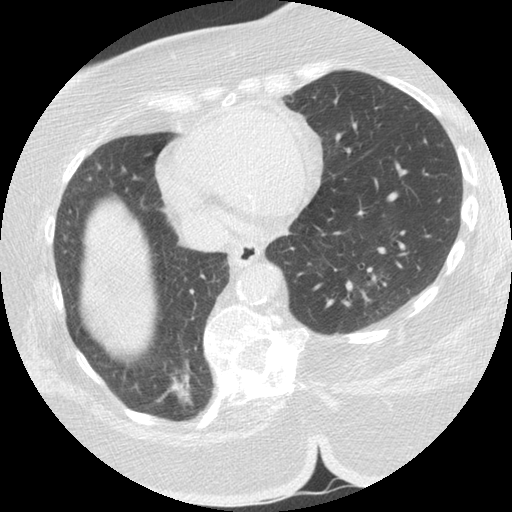
Low-dose screening chest CT, one axial slice; position 52 of 151 along the scan axis; reconstruction kernel STANDARD; lung window (W 1500 / L -600 HU); 2.5 mm slice thickness; 512 × 512 image matrix, field of view 340 × 340 mm.
Outlined on this slice (expert manual segmentation):
- lesion 1 (tumor, lower lobe of right lung): bounding box [x1, y1, x2, y2] px = [170, 371, 193, 406]